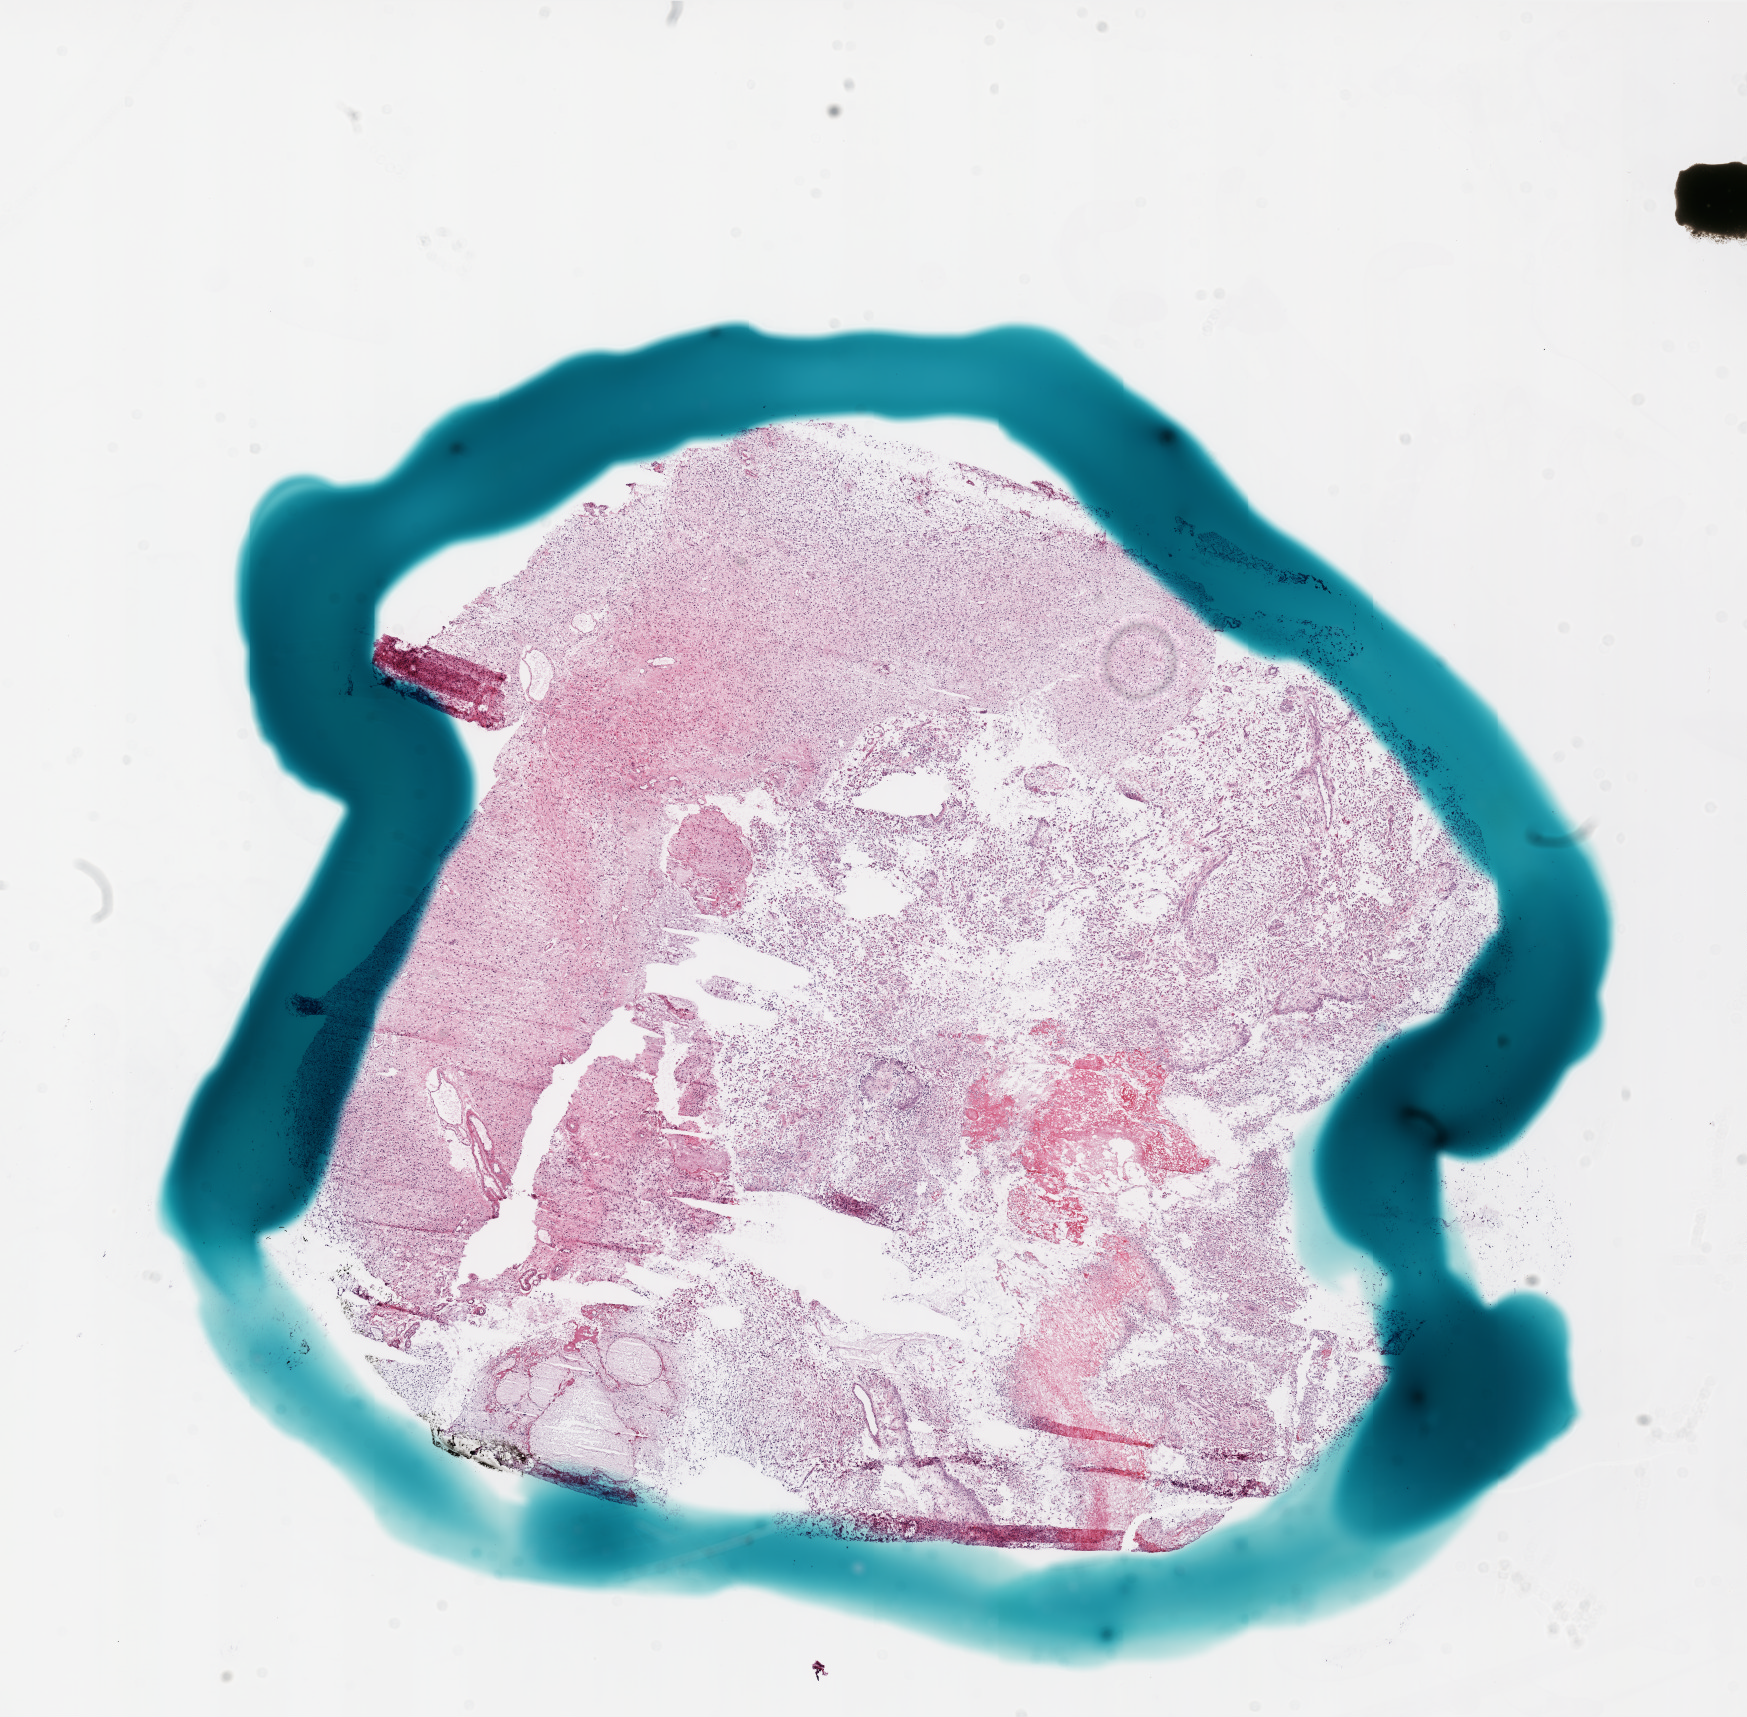
Digitized Hematoxylin and eosin (H&E) stained tissue section (whole slide), whole scanned area (about 14.0 x 13.7 mm, from a 20x scan) shown as a low-resolution overview, frozen section from the bottom of the tissue portion, brain, primary tumour sample. Patient: male, age at initial diagnosis 66 years. Slide review estimates, as recorded: tumour cells 90%, tumour nuclei 95%, normal cells 0%, stromal cells 0%, necrosis 10%.
* diagnosis: Glioblastoma